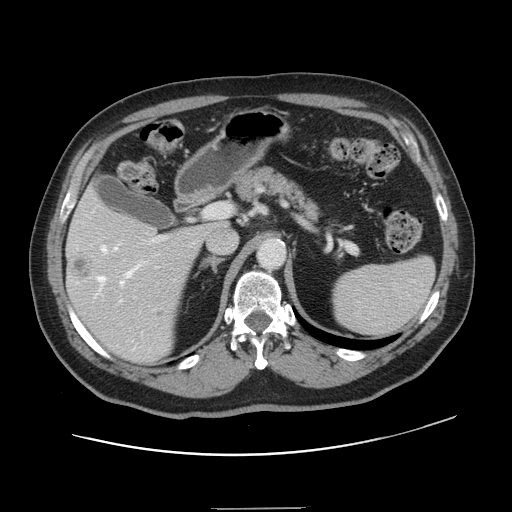
Contrast-enhanced abdominal CT, one axial slice; position 85 of 143 along the scan axis; 120 kVp; soft-tissue window (W 400 / L 40 HU); 512 × 512 image matrix, field of view 402 × 402 mm. Male patient, age 62 years. From the clinical record (not read from this slice): diagnosis: colorectal cancer liver metastases, imaged before liver resection; multiple liver metastases: yes; largest metastasis: 2.7 cm; disease in both lobes: no.
Annotated regions visible in this slice (expert manual segmentation):
- hepatic veins: bounding box <98,246,140,292> (left, top, right, bottom; pixels)
- liver: <67,190,216,363>
- planned liver remnant (the part of the liver to remain after resection): <69,189,218,240>
- portal vein (with intrahepatic branches): <120,205,220,302>
- liver metastasis: <70,253,93,280>